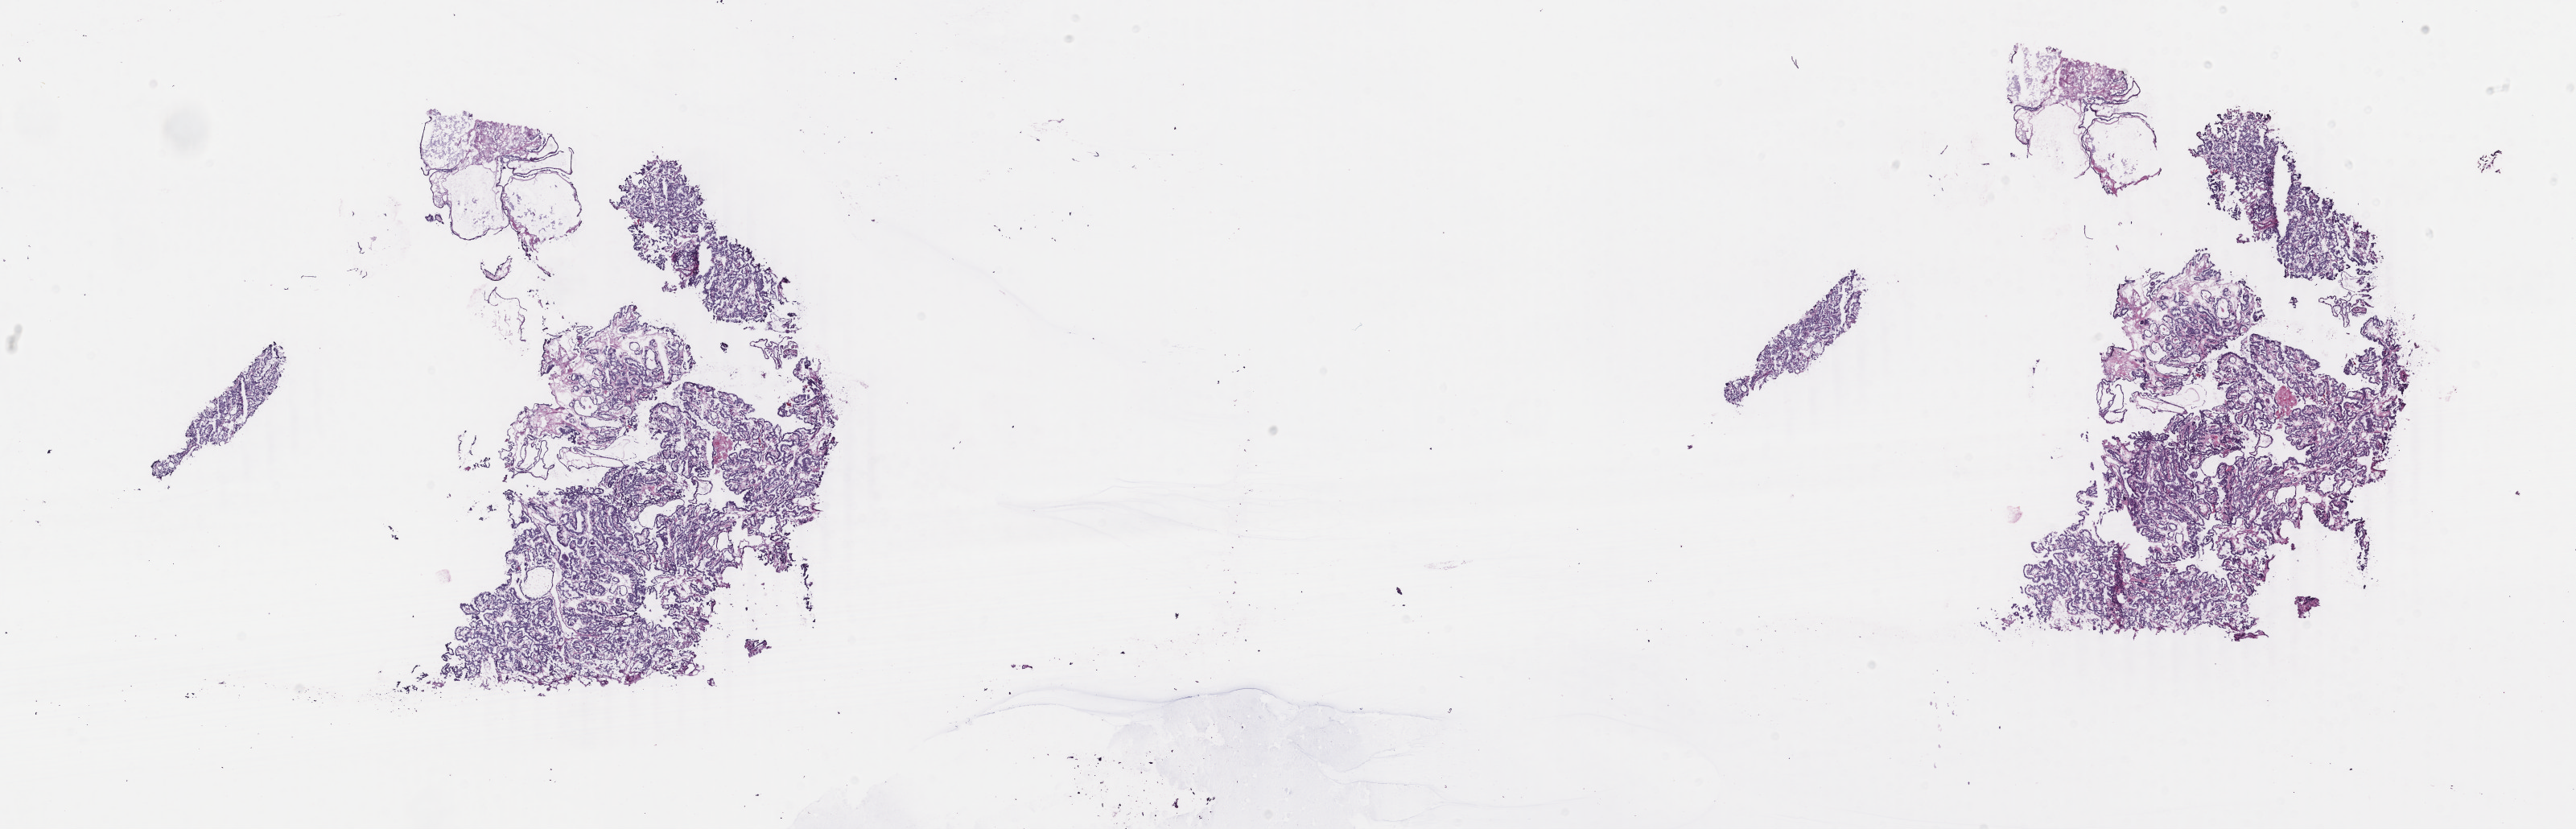
Hematoxylin and eosin (H&E) stained whole-slide image — a low-resolution overview of the entire scanned area, about 25.5 x 8.2 mm (acquisition: 40x scan). Frozen section from the bottom of the tissue portion. Thyroid, primary tumour sample. Patient: female, age at initial diagnosis 37 years. Slide review estimates, as recorded: tumour cells 100%, tumour nuclei 95%, normal cells 0%, stromal cells 0%, necrosis 0%. Inflammatory infiltration, as recorded: lymphocyte infiltration 0%, monocyte infiltration 0%, neutrophil infiltration 0%.
Laterality: right. Lymph nodes positive (case pathology): 0 of 7 examined. Pathologic diagnosis: Papillary adenocarcinoma, NOS. AJCC pathologic stage: I. TNM: T2 N0 M0.